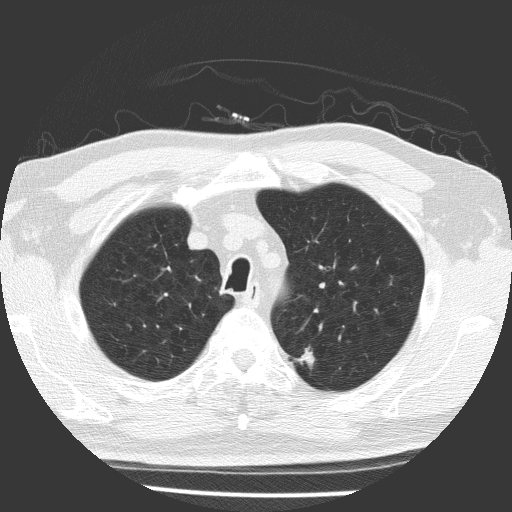
Low-dose screening chest CT, one axial slice. Slice 135 of 169 in the series (ordered by position). Reconstruction kernel FC51. Lung window (W 1500 / L -600 HU). 2 mm slice thickness. 512 × 512 image matrix, field of view 323 × 323 mm.
Annotated regions visible in this slice (outlined manually by an expert reader):
- lesion 1 (tumor, upper lobe of left lung): bounding box <295,346,315,369> (left, top, right, bottom; pixels)